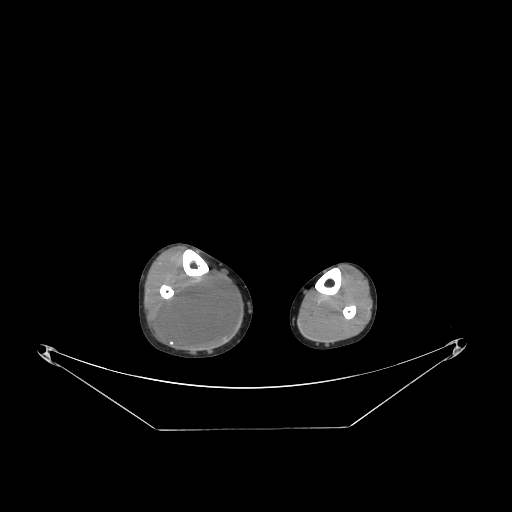
CT of an extremity soft-tissue mass (from a PET/CT study), one axial slice; slice 88 of 267 in the series (ordered by position); reconstruction kernel STANDARD; 140 kVp; soft-tissue window (W 400 / L 40 HU); 3.75 mm slice thickness; 512 × 512 image matrix. Male patient. Case-level facts recorded for this patient, not image findings: histological type: liposarcoma - round cell; grade: high; site of the primary tumour: right calf.
Outlined on this slice (expert contour drawn on MRI and transferred to this co-registered scan by the dataset authors):
- gross tumour volume (mass): box from (x=158, y=274) to (x=238, y=348) px